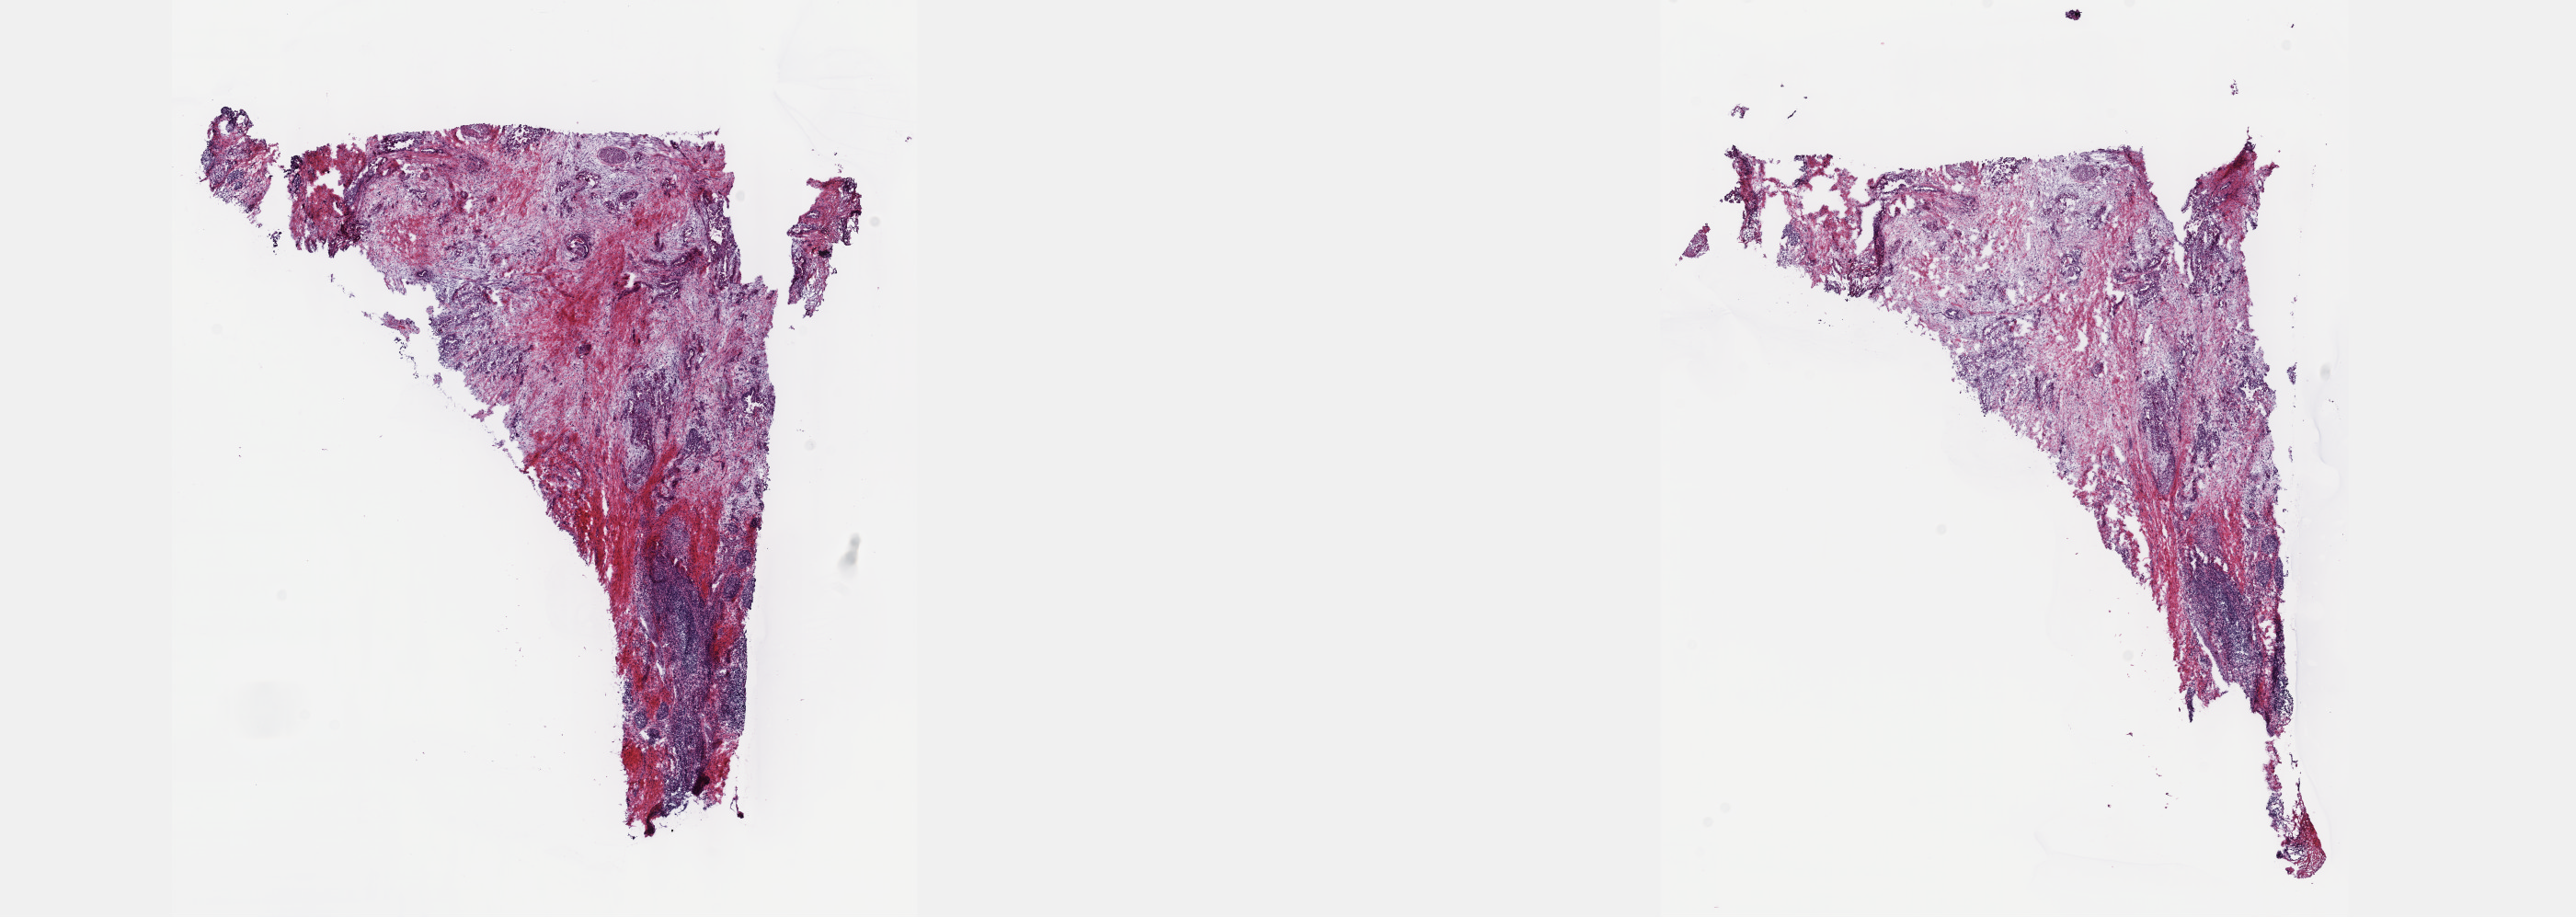
Hematoxylin and eosin (H&E) stained whole-slide image, whole scanned area (about 22.6 x 8.1 mm) shown as a low-resolution overview. Frozen section from the top of the tissue portion. Sample: primary tumour, pancreas. Patient: male, age at initial diagnosis 43 years. Histologic grade: G2 (moderately differentiated). Composition of this section per pathologist review: tumour cells 35%, tumour nuclei 35%, normal cells 5%, stromal cells 60%, necrosis 0%. Inflammatory infiltration, as recorded: lymphocyte infiltration 12%, monocyte infiltration 2%, neutrophil infiltration 10%.
Histologic diagnosis: Infiltrating duct carcinoma, NOS (head of pancreas). Lymph nodes positive (case pathology): 8 of 16 examined. AJCC pathologic stage: IIB. TNM: T3 N1 M0.